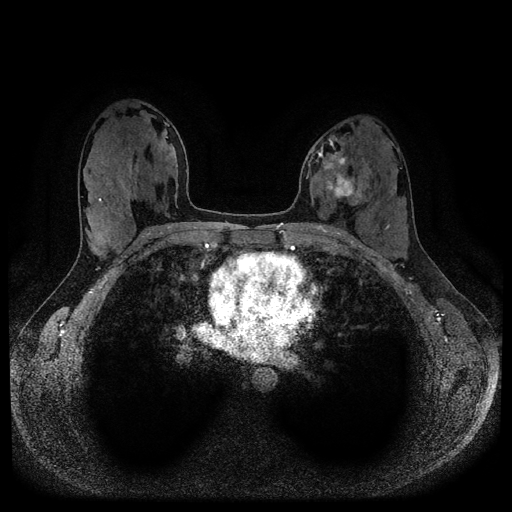
Breast MRI (dynamic contrast-enhanced, multi-phase), one axial slice; slice 56 of 116 in the series (ordered by position); dynamic contrast-enhanced series, time point 2 of 5 at this slice position (early post-contrast); 1.5 T; TE 2.6 ms, TR 5.3 ms; 512 × 512 image matrix, field of view 350 × 350 mm. Patient: female, 33 years.
Structures marked on this image (semi-automatically segmented with operator editing):
- breast lesion (labelled 'tumour' in the annotation; benign lesions carry a separate 'benign' label): bounding box [x1, y1, x2, y2] px = [321, 151, 357, 202]